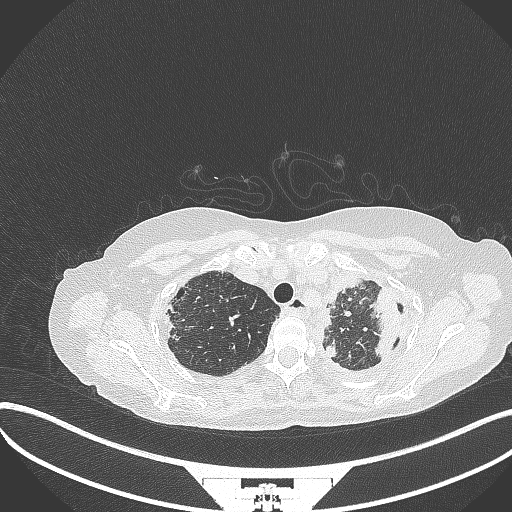
Chest CT, one axial slice; position 286 of 373 along the scan axis; 120 kVp; lung window (W 1500 / L -600 HU); 1 mm slice thickness; 512 × 512 image matrix, field of view 400 × 400 mm. Patient: female, 56 years. Case-level facts recorded for this patient, not image findings: clinical TNM (as recorded): T1 N0 M0.
Structures marked on this image (rectangle marked by the reading radiologist):
- lung tumour (recorded histology: adenocarcinoma): box from (x=366, y=285) to (x=407, y=365) px